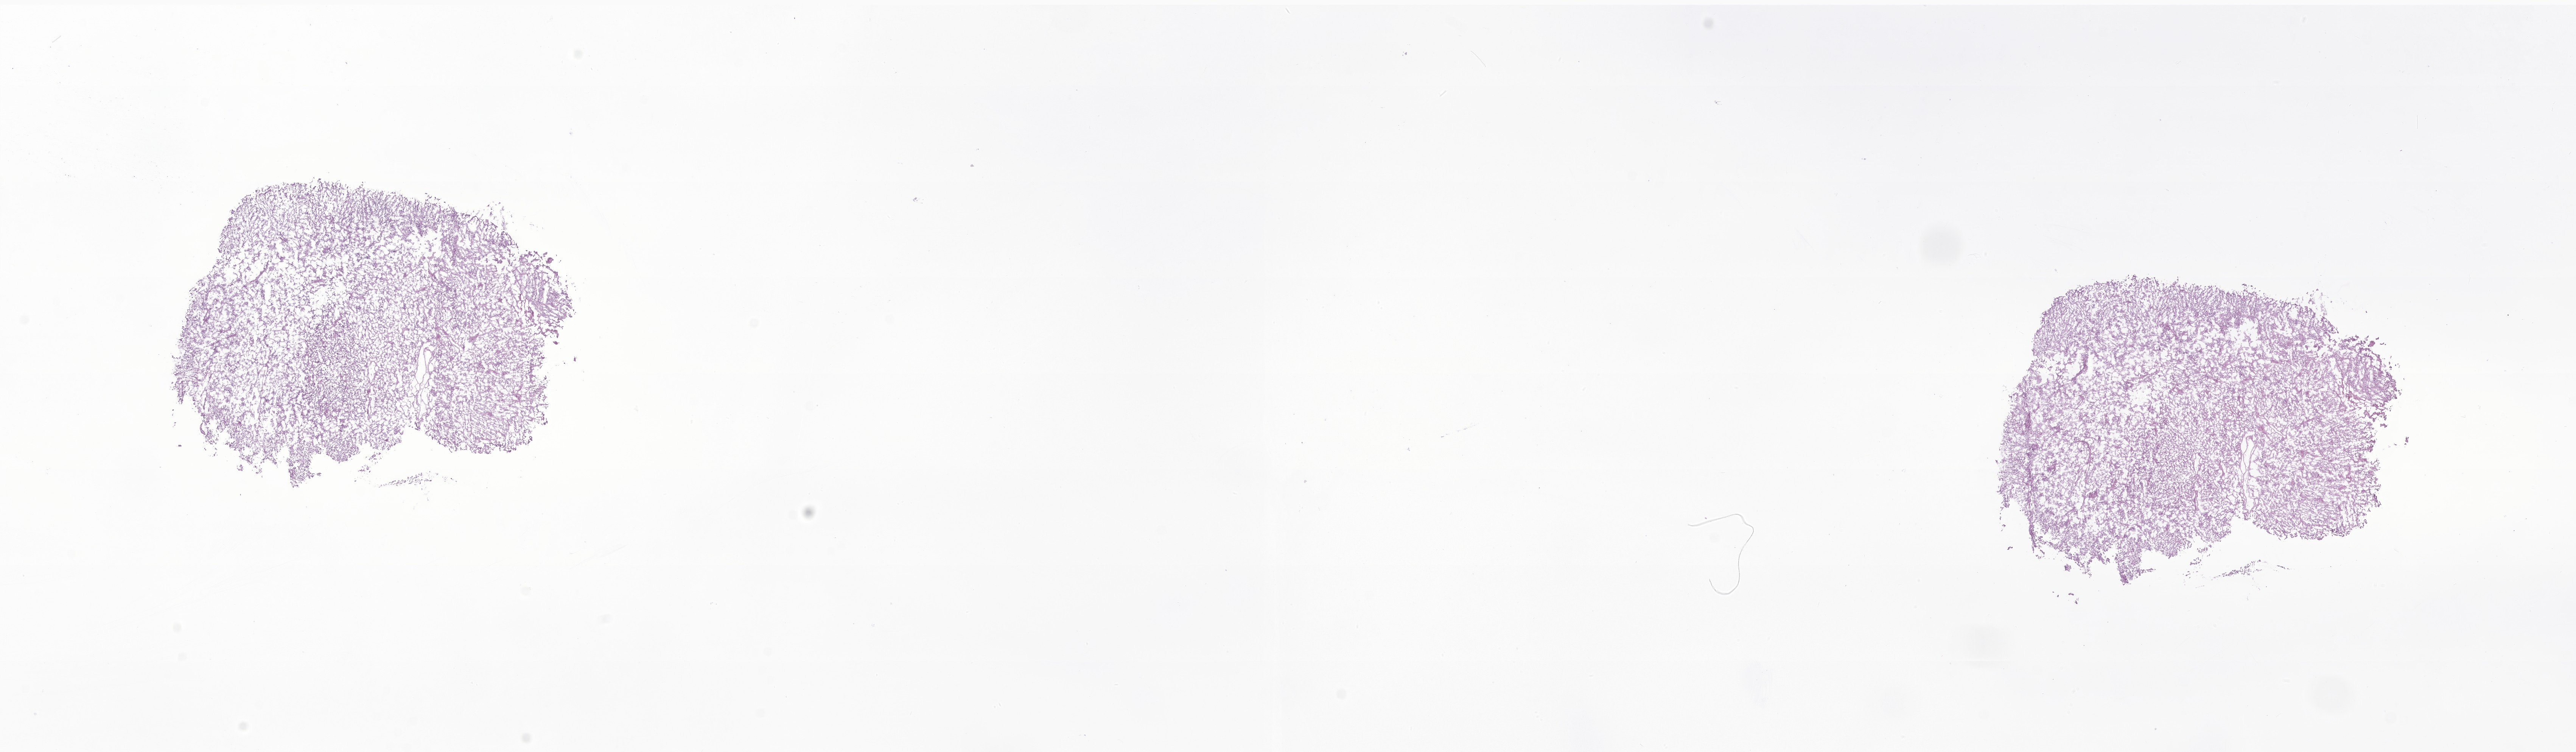
Digitized hematoxylin and eosin (H&E)-stained section of tumor tissue from the brain, shown as a low-resolution overview of the whole scanned area (about 28.7 x 8.4 mm), frozen section (OCT-embedded). Female patient, age 82 months (6 years 10 months).
Diagnosis (ICD-O-3 morphology term): Glioma, malignant.